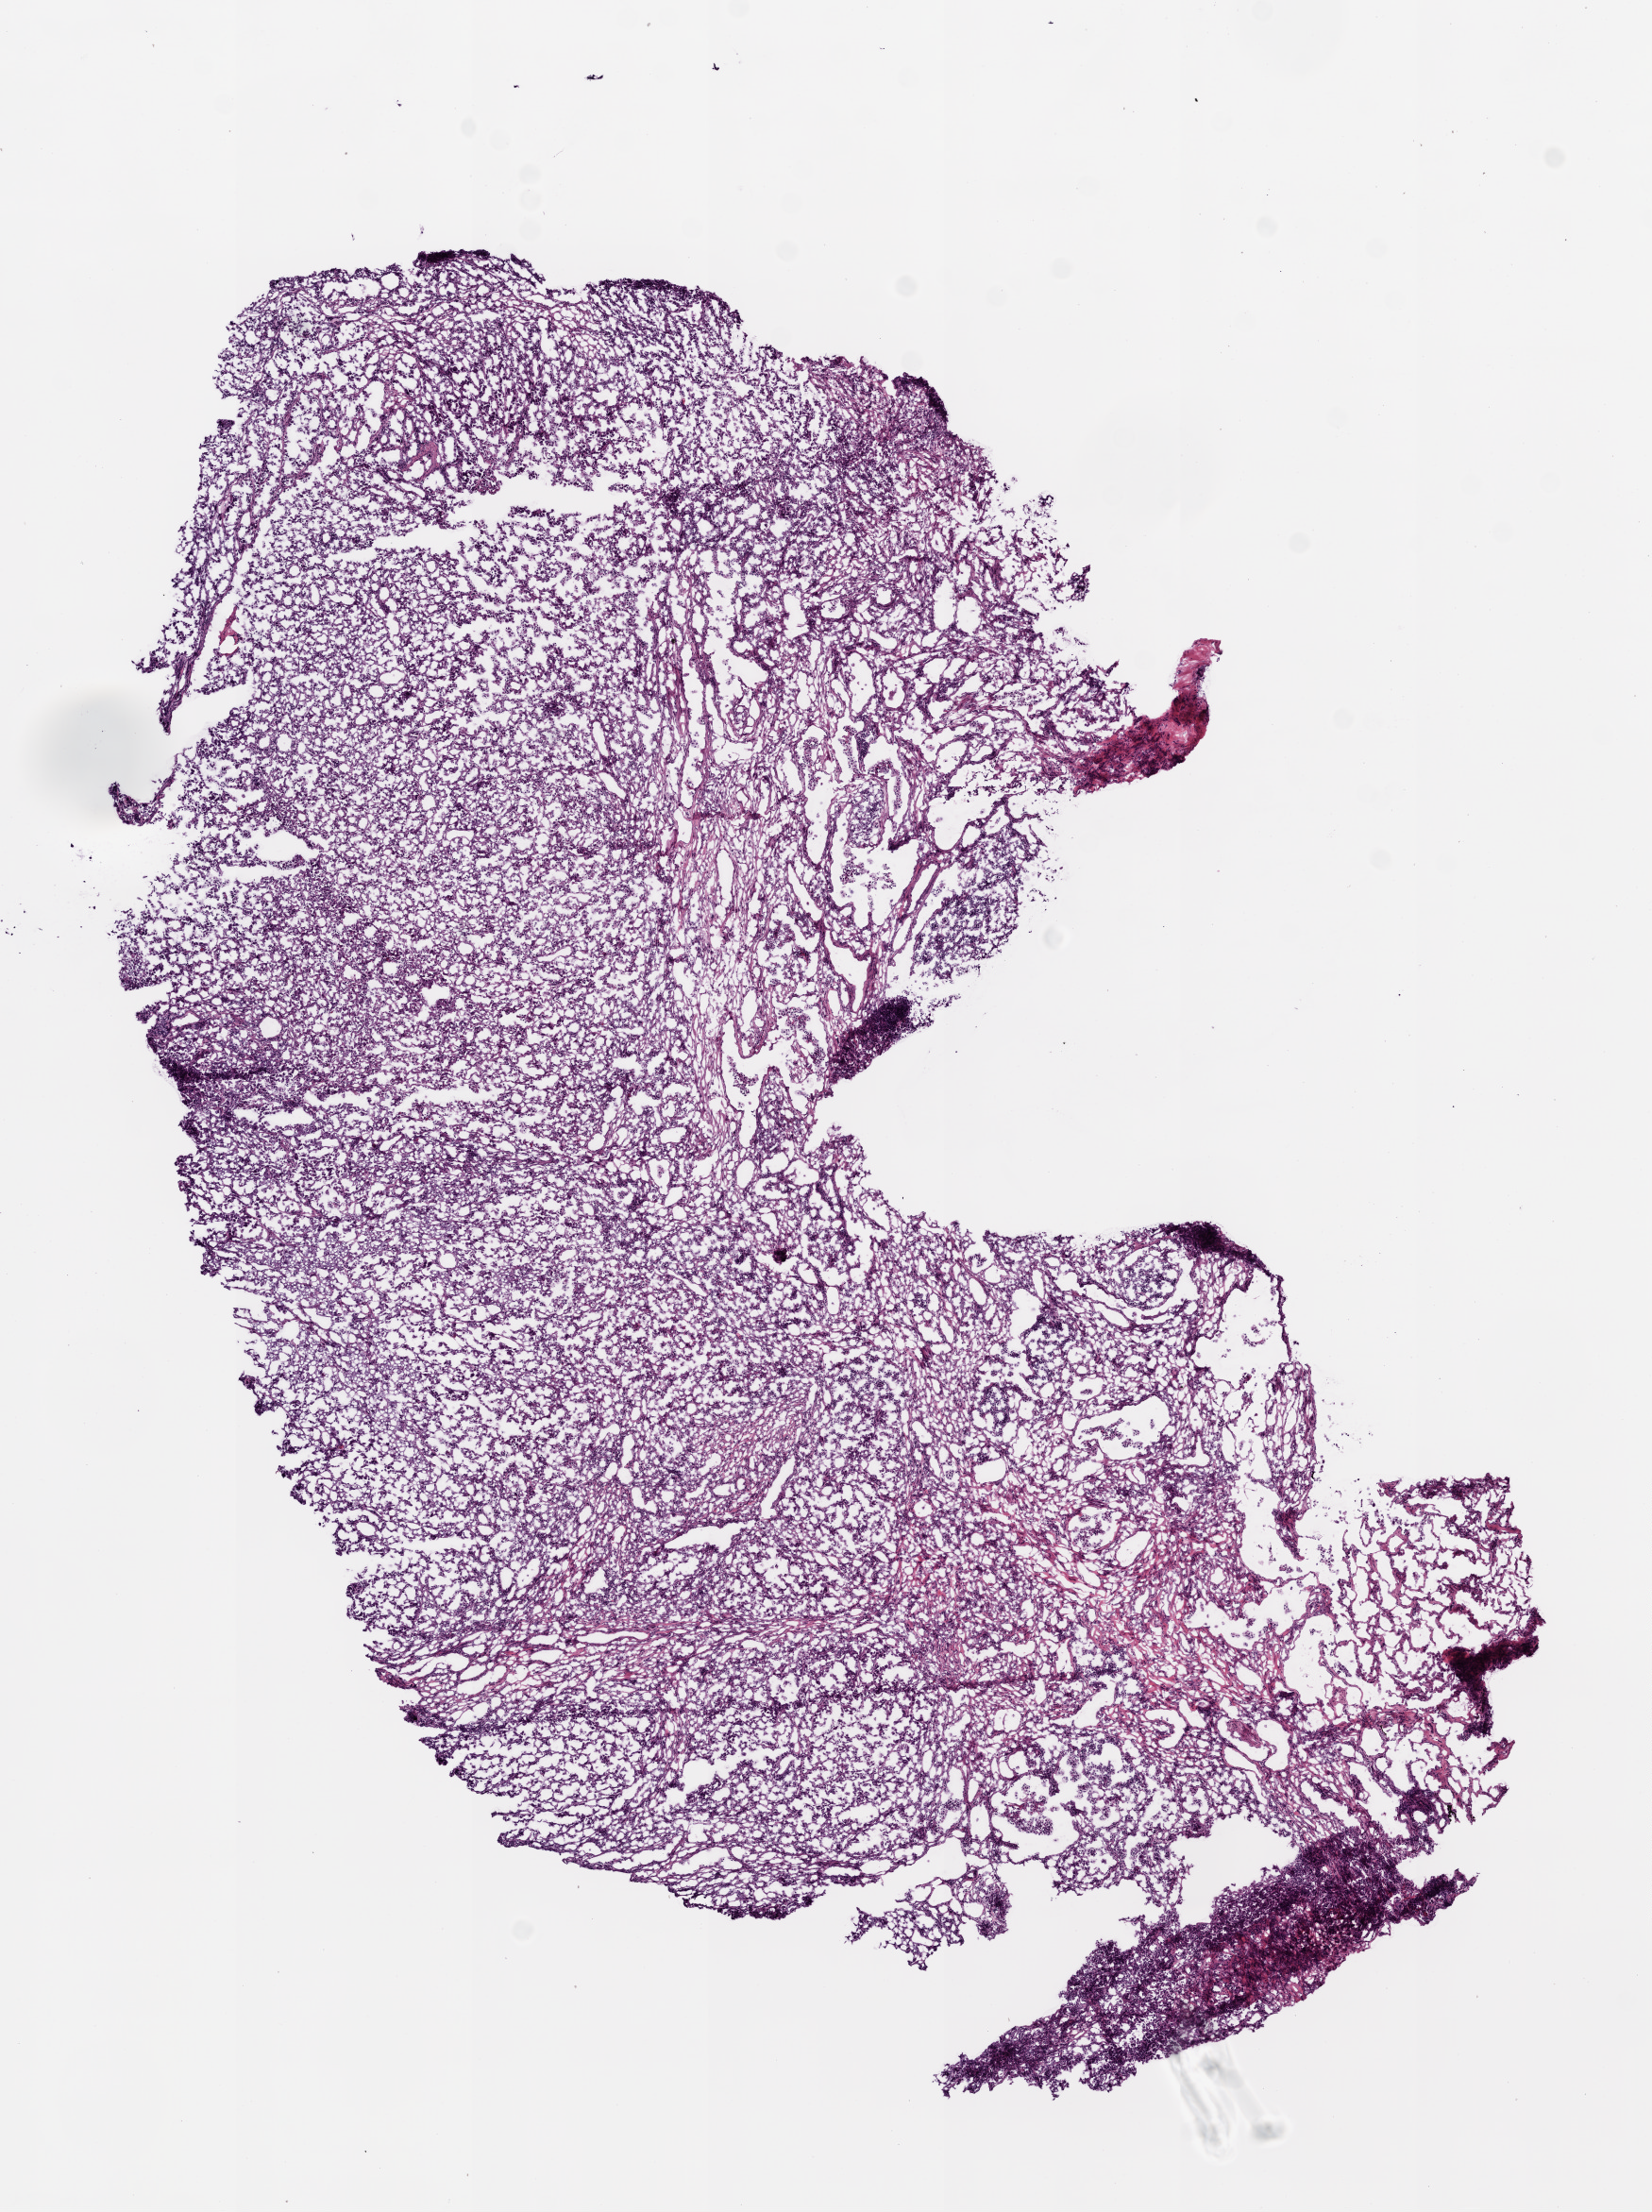
Digitized H&E-stained tissue section (whole slide), low-resolution overview of the scanned area, about 7.0 x 9.4 mm (from a 20x scan); frozen section; lung, primary tumour sample. Patient: female, age at initial diagnosis 73 years. Composition of this section per pathologist review: tumour cells 95%, tumour nuclei 70%, normal cells 0%, stromal cells 5%, necrosis 0%.
Histologic diagnosis: Adenocarcinoma, NOS. AJCC pathologic stage: IIIA.